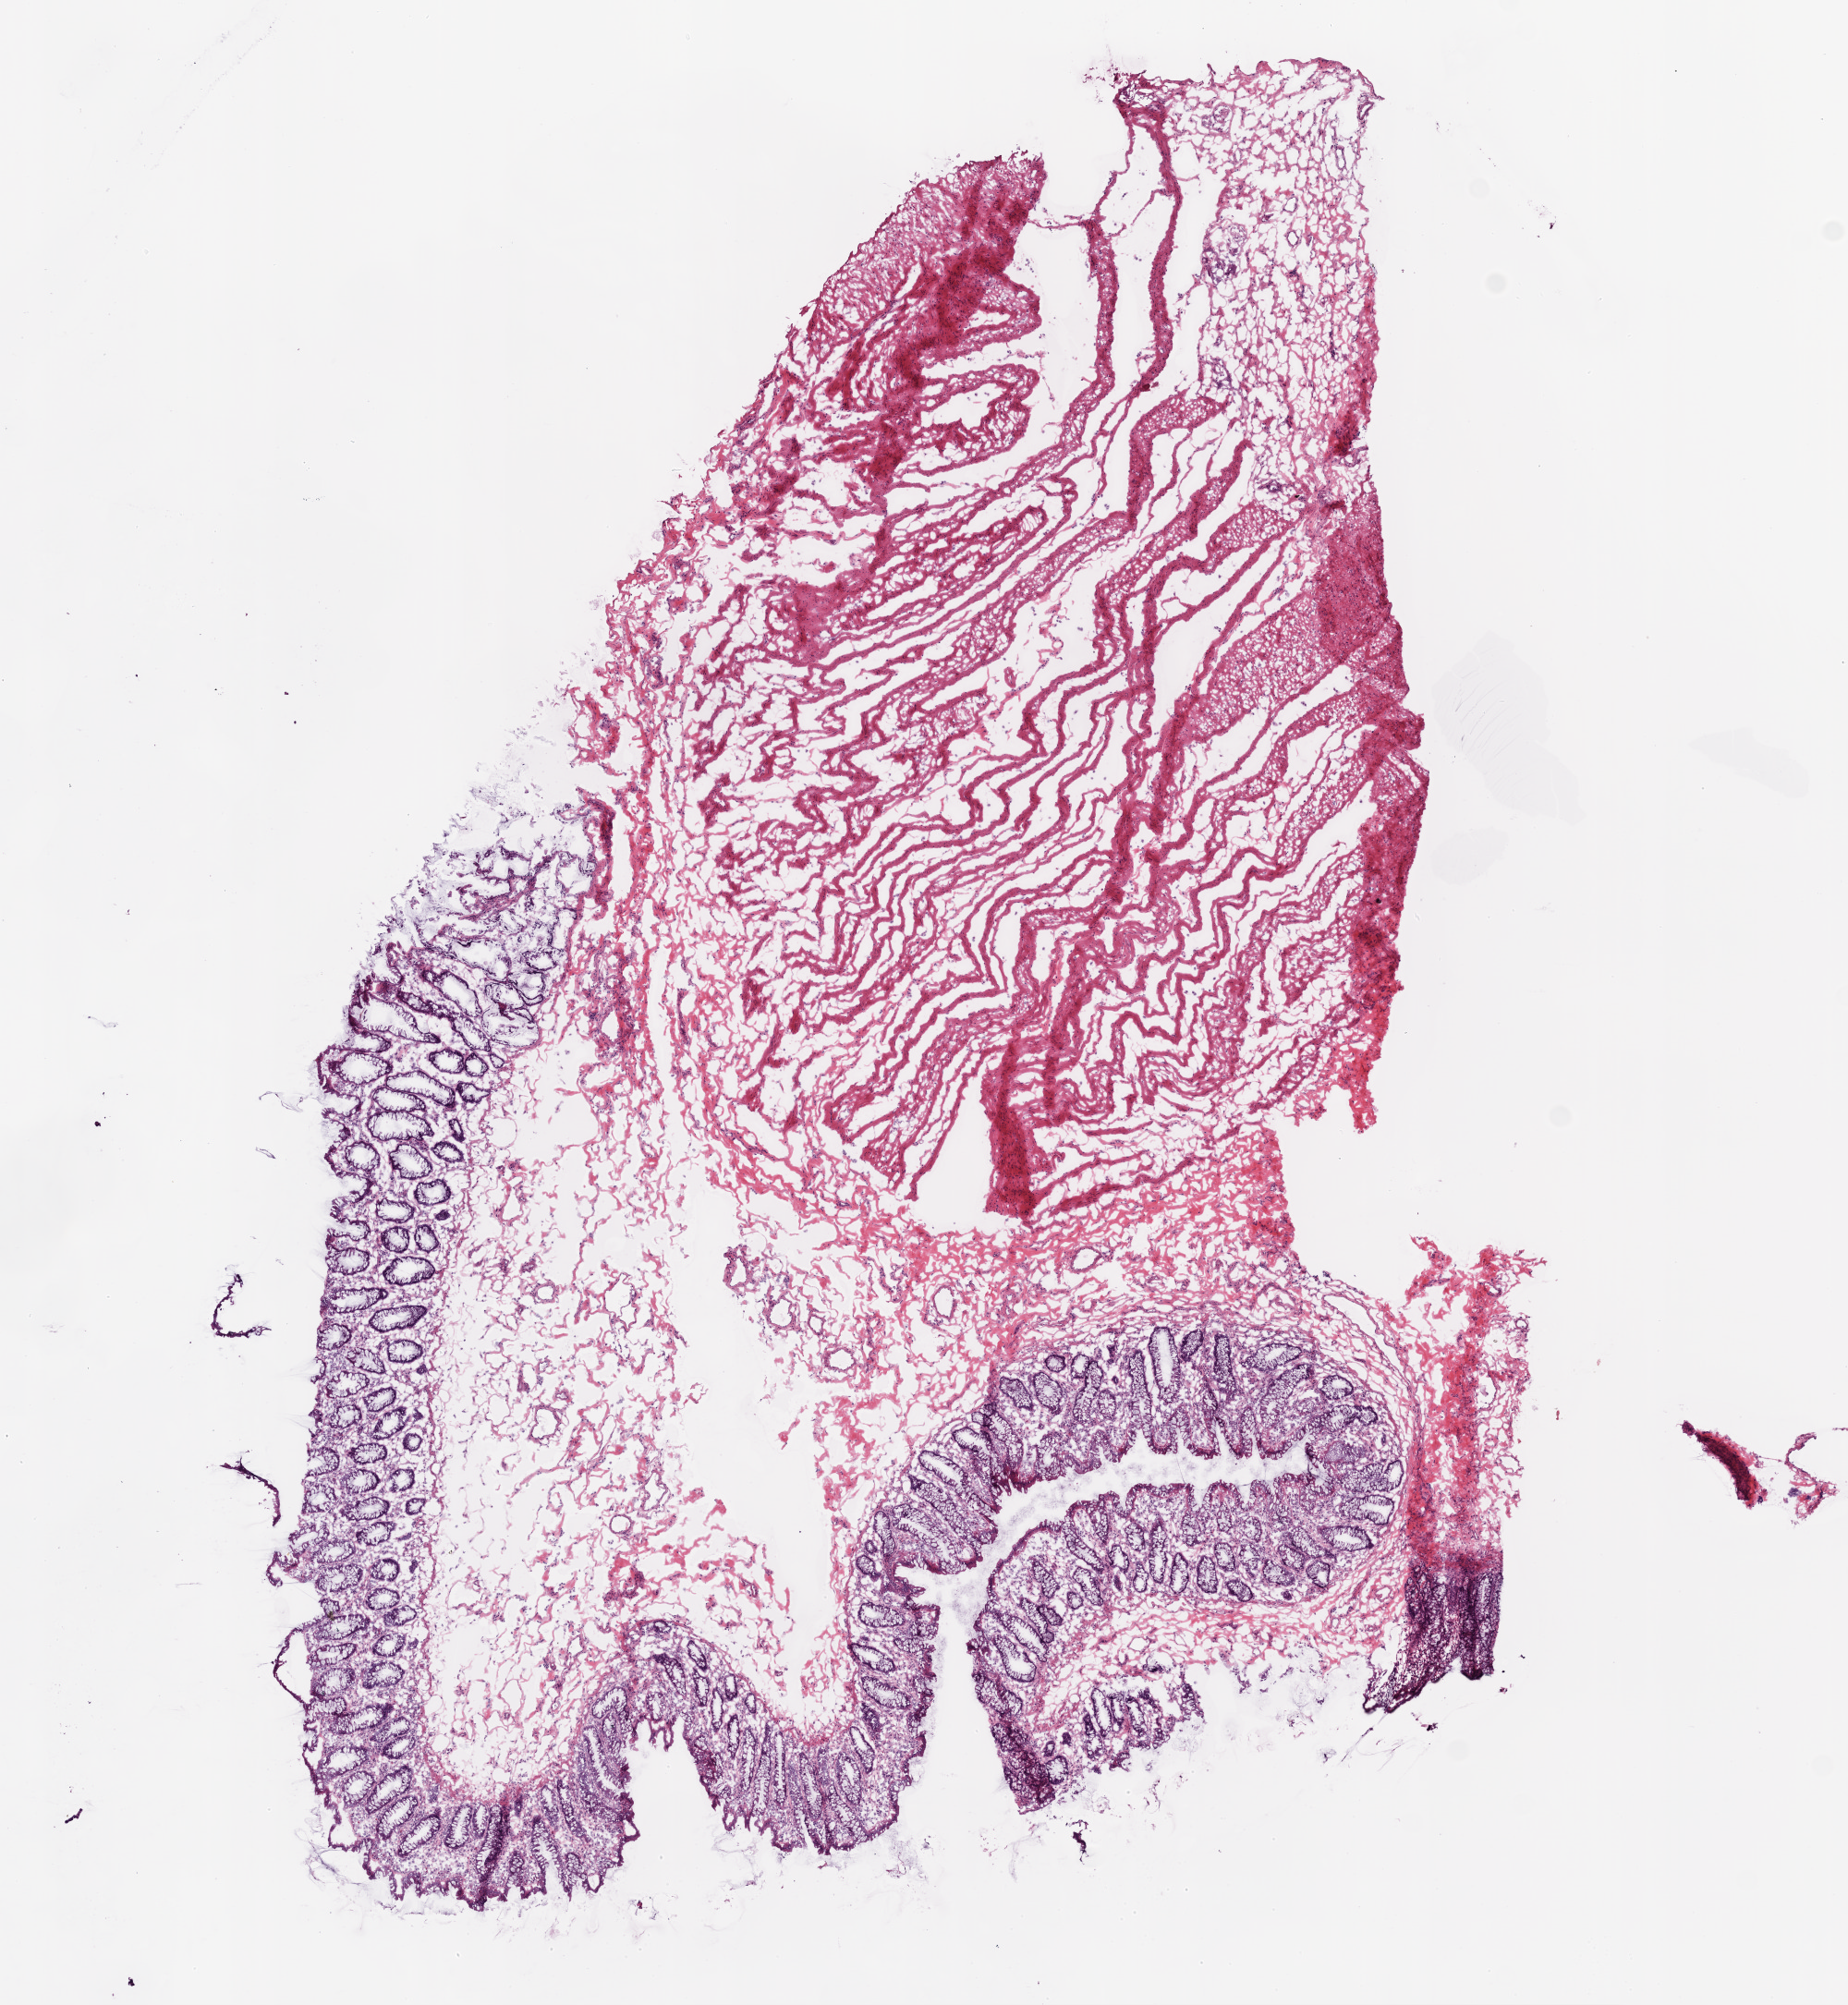
H&E whole-slide image, whole scanned area (about 8.0 x 8.7 mm) shown as a low-resolution overview. Frozen section from the bottom of the tissue portion. Sample: solid tissue normal (non-tumour tissue), ovary. Female, age 76 years at initial diagnosis.
This section: solid tissue normal (non-tumour) sample from the same patient. Patient diagnosis: Serous cystadenocarcinoma, NOS.